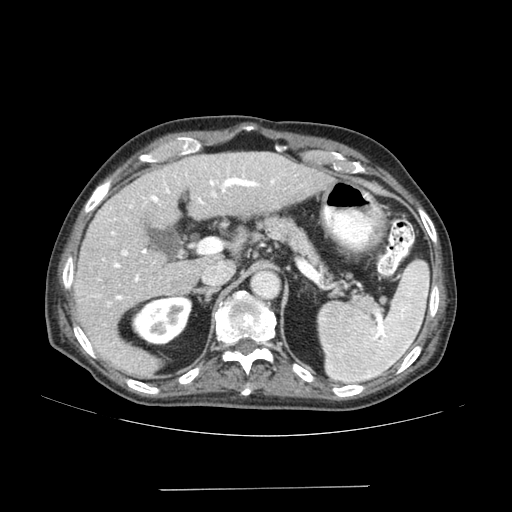
Contrast-enhanced abdominal CT (liver protocol), one axial slice; reconstruction kernel SOFT; 120 kVp; soft-tissue window (W 400 / L 40 HU); 2.5 mm slice thickness; 512 × 512 image matrix. Case-level facts recorded for this patient, not image findings: diagnosis: hepatocellular carcinoma (patient treated with transarterial chemoembolisation; whether this scan precedes or follows treatment is not stated here); TNM stage (as recorded): Stage-IVA; Child-Pugh class: A; tumour differentiation: poorly differentiated.
Annotated regions visible in this slice (semi-automatically segmented with operator editing):
- liver parenchyma outside the tumour (the mass and vessels are separate outlines, so this box may not span the whole liver): bounding box <74,152,332,377> (left, top, right, bottom; pixels)
- liver vessels: <109,175,275,304>